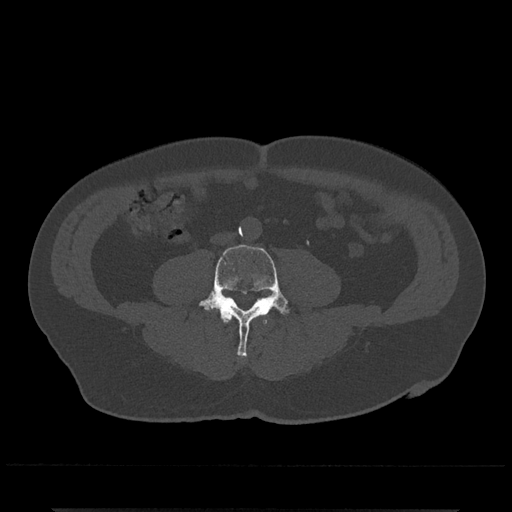
CT including the spine, one axial slice. Position 151 of 797 along the scan axis. Reconstruction kernel Br40s/3. Bone window (W 1800 / L 400 HU). 0.5 mm slice thickness. 512 × 512 image matrix. Male patient, age 67 years. Case-level facts recorded for this patient, not image findings: primary cancer: prostate.
Annotated regions visible in this slice (semi-automatically segmented with operator editing):
- L3 vertebra: bounding box (x1, y1, x2, y2) in pixels: (223, 316, 267, 324)
- L4 vertebra: (199, 244, 290, 357)